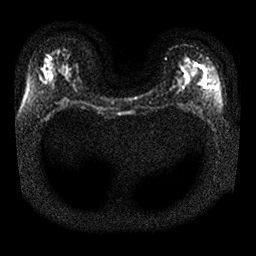
Breast MRI, one axial slice. Slice 16 of 25 in the series (ordered by position). Diffusion-weighted series; image 2 of 4 stored at this slice position (different b-values; order by instance number). 1.5 T. 4 mm slice thickness. 256 × 256 image matrix, field of view 340 × 340 mm. Female patient.
Annotated regions visible in this slice (outlined manually by an expert reader):
- tumour on diffusion-weighted imaging: box from (x=45, y=69) to (x=53, y=79) px